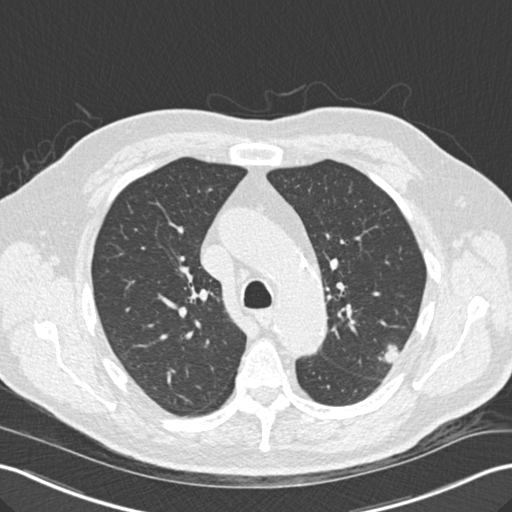
Chest CT (low-dose screening protocol), one axial image; third annual screen; lung window (W 1500 / L -600 HU); 2 mm slice thickness; 512 × 512 image matrix, field of view 354 × 354 mm. Male participant, aged 67 years at enrolment.
• Expert reader's lesion annotation, box from (x=365, y=334) to (x=409, y=372) px.
• The screening reader recorded 2 non-calcified nodules or masses ≥4 mm on this exam (left upper lobe, left lower lobe); which of them this box marks is not recorded.
• Official screen result: positive, other.
• Later outcome: lung cancer diagnosed 55 days after this screen — squamous cell carcinoma, large cell, nonkeratinizing, NOS, left upper lobe, moderately differentiated (G2), stage IA (AJCC 6th edition), 15 mm at pathology.